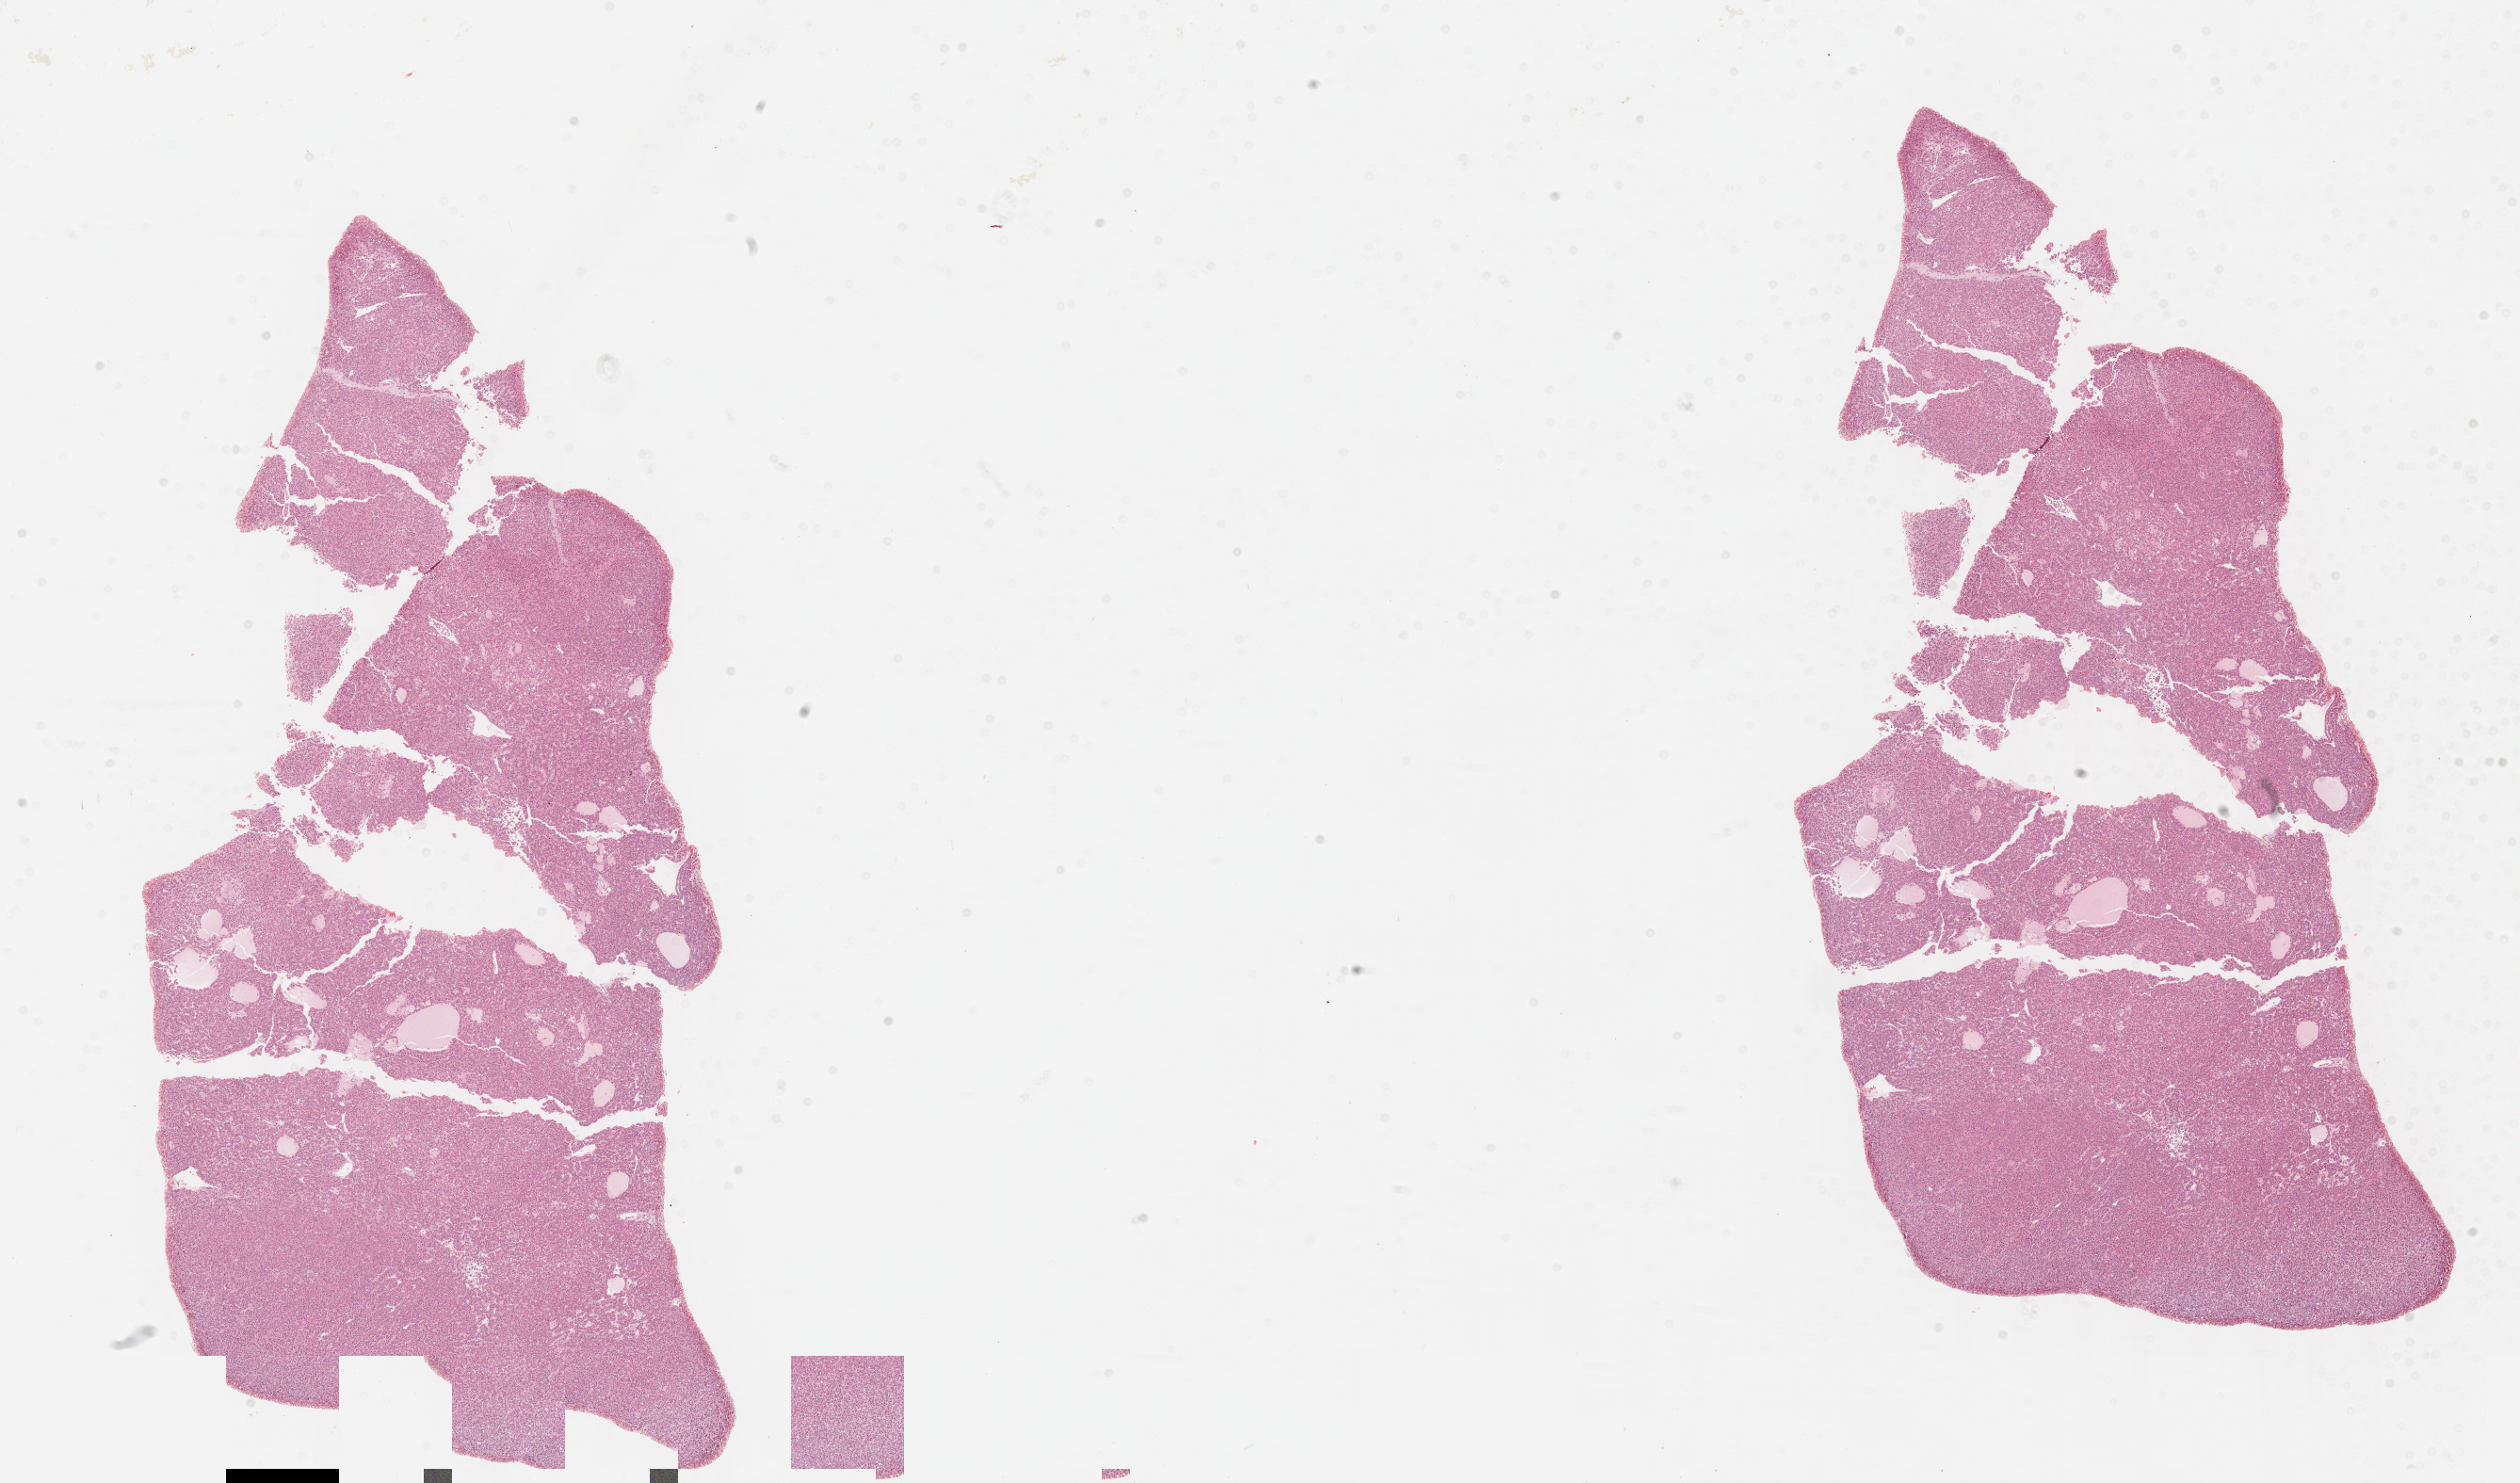
Digitized H&E-stained tissue section (whole slide), a low-resolution overview of the entire scanned area, about 21.6 x 12.7 mm, formalin-fixed paraffin-embedded (FFPE) diagnostic section, primary tumour sample from the liver. Patient: male, age at initial diagnosis 61 years. Histologic grade: G3 (poorly differentiated).
- diagnosis: Hepatocellular carcinoma, NOS
- AJCC pathologic stage: I